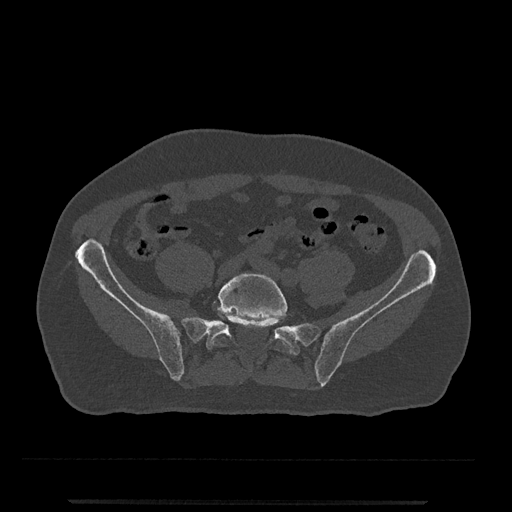
CT including the spine, one axial slice. Slice 44 of 797 in the series (ordered by position). Reconstruction kernel Br40s/3. 120 kVp. Bone window (W 1800 / L 400 HU). 512 × 512 image matrix. Male patient, age 63 years. From the clinical record (not read from this slice): primary cancer: prostate.
Outlined on this slice (semi-automatically segmented with operator editing):
- L5 vertebra: box from (x=209, y=273) to (x=289, y=352) px